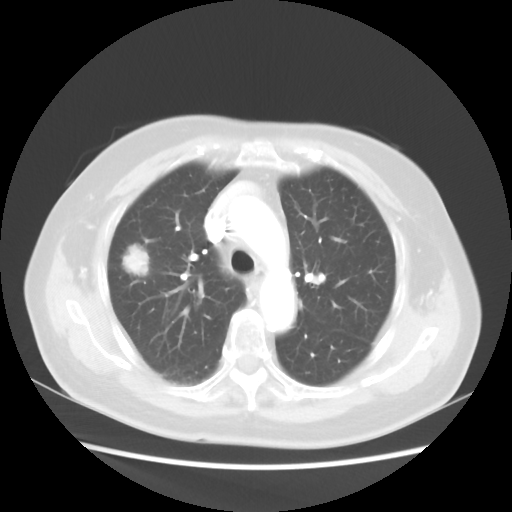
Chest CT, one axial slice; slice 33 of 48 in the series (ordered by position); reconstruction kernel STANDARD; 100 kVp; lung window (W 1500 / L -600 HU); 512 × 512 image matrix, field of view 360 × 360 mm. Patient: female, 75 years. Case-level facts recorded for this patient, not image findings: clinical TNM (as recorded): T1c N0 M0.
Annotated regions visible in this slice (bounding box drawn by a radiologist):
- lung tumour (recorded histology: adenocarcinoma): bounding box [x1, y1, x2, y2] px = [122, 246, 152, 277]